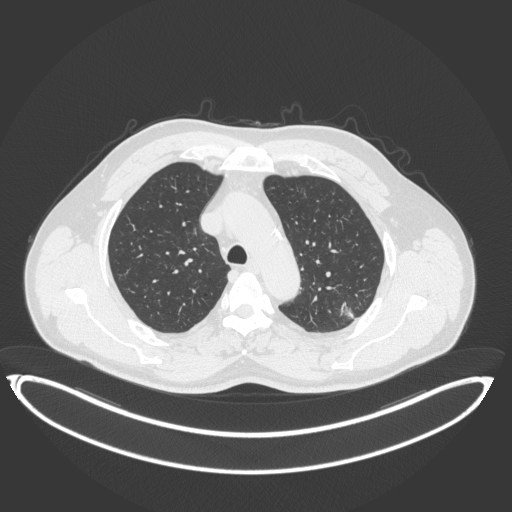
Chest CT, one axial slice. Slice 273 of 399 in the series (ordered by position). Reconstruction kernel B31f. 120 kVp. Lung window (W 1500 / L -600 HU). 512 × 512 image matrix. Patient: male, 58 years. From the clinical record (not read from this slice): clinical TNM (as recorded): T1c N0 M0; histopathological grade: G1-2.
Annotated regions visible in this slice (rectangle marked by the reading radiologist):
- lung tumour (recorded histology: adenocarcinoma): bounding box <340,300,362,324> (left, top, right, bottom; pixels)